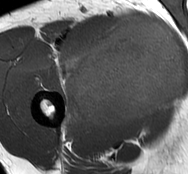
MRI of an extremity soft-tissue mass, one axial slice; slice 46 of 93 in the series (ordered by position); MR volume resampled by the dataset authors to the PET/CT grid (not the native acquisition matrix); 3.27 mm slice thickness; 188 × 174 image matrix, field of view 184 × 170 mm. Male patient. From the clinical record (not read from this slice): histological type: undifferentiated - pleiomorphic; grade: high; site of the primary tumour: right thigh.
Structures marked on this image (expert contour drawn on MRI and transferred to this co-registered scan by the dataset authors):
- gross tumour volume including surrounding oedema: bounding box <61,17,185,130> (left, top, right, bottom; pixels)
- gross tumour volume (mass): <70,19,185,127>